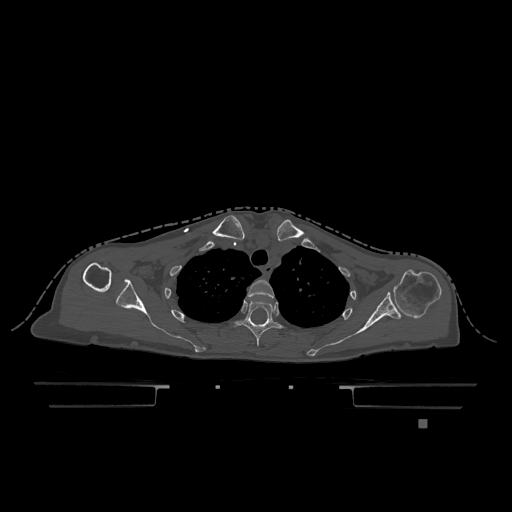
CT including the spine, one axial slice; slice 930 of 1317 in the series (ordered by position); bone window (W 1800 / L 400 HU); 512 × 512 image matrix. Female patient, age 74 years. Case-level facts recorded for this patient, not image findings: primary cancer: lung.
Annotated regions visible in this slice (semi-automatic segmentation, software-assisted and operator-edited):
- T2 vertebra: bounding box <247,279,274,298> (left, top, right, bottom; pixels)
- T3 vertebra: <233,300,282,346>